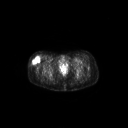
FDG PET of an extremity soft-tissue mass (from a PET/CT study), one axial slice. Position 57 of 267 along the scan axis. 3.27 mm slice thickness. 128 × 128 image matrix. Patient: female, 34 years. From the clinical record (not read from this slice): histological type: synovial sarcoma; grade: intermediate; site of the primary tumour: right thigh.
Structures marked on this image (expert contour drawn on MRI and transferred to this co-registered scan by the dataset authors):
- gross tumour volume including surrounding oedema: bounding box <31,56,40,64> (left, top, right, bottom; pixels)
- gross tumour volume (mass): <31,56,40,65>